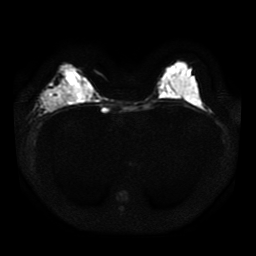
Breast MRI, one axial slice. Slice 17 of 41 in the series (ordered by position). Diffusion-weighted series; image 2 of 4 stored at this slice position (different b-values; order by instance number). 1.5 T. 256 × 256 image matrix, field of view 330 × 330 mm. Female patient.
Structures marked on this image (manually delineated by an expert):
- tumour on diffusion-weighted imaging: bounding box <39,87,76,112> (left, top, right, bottom; pixels)